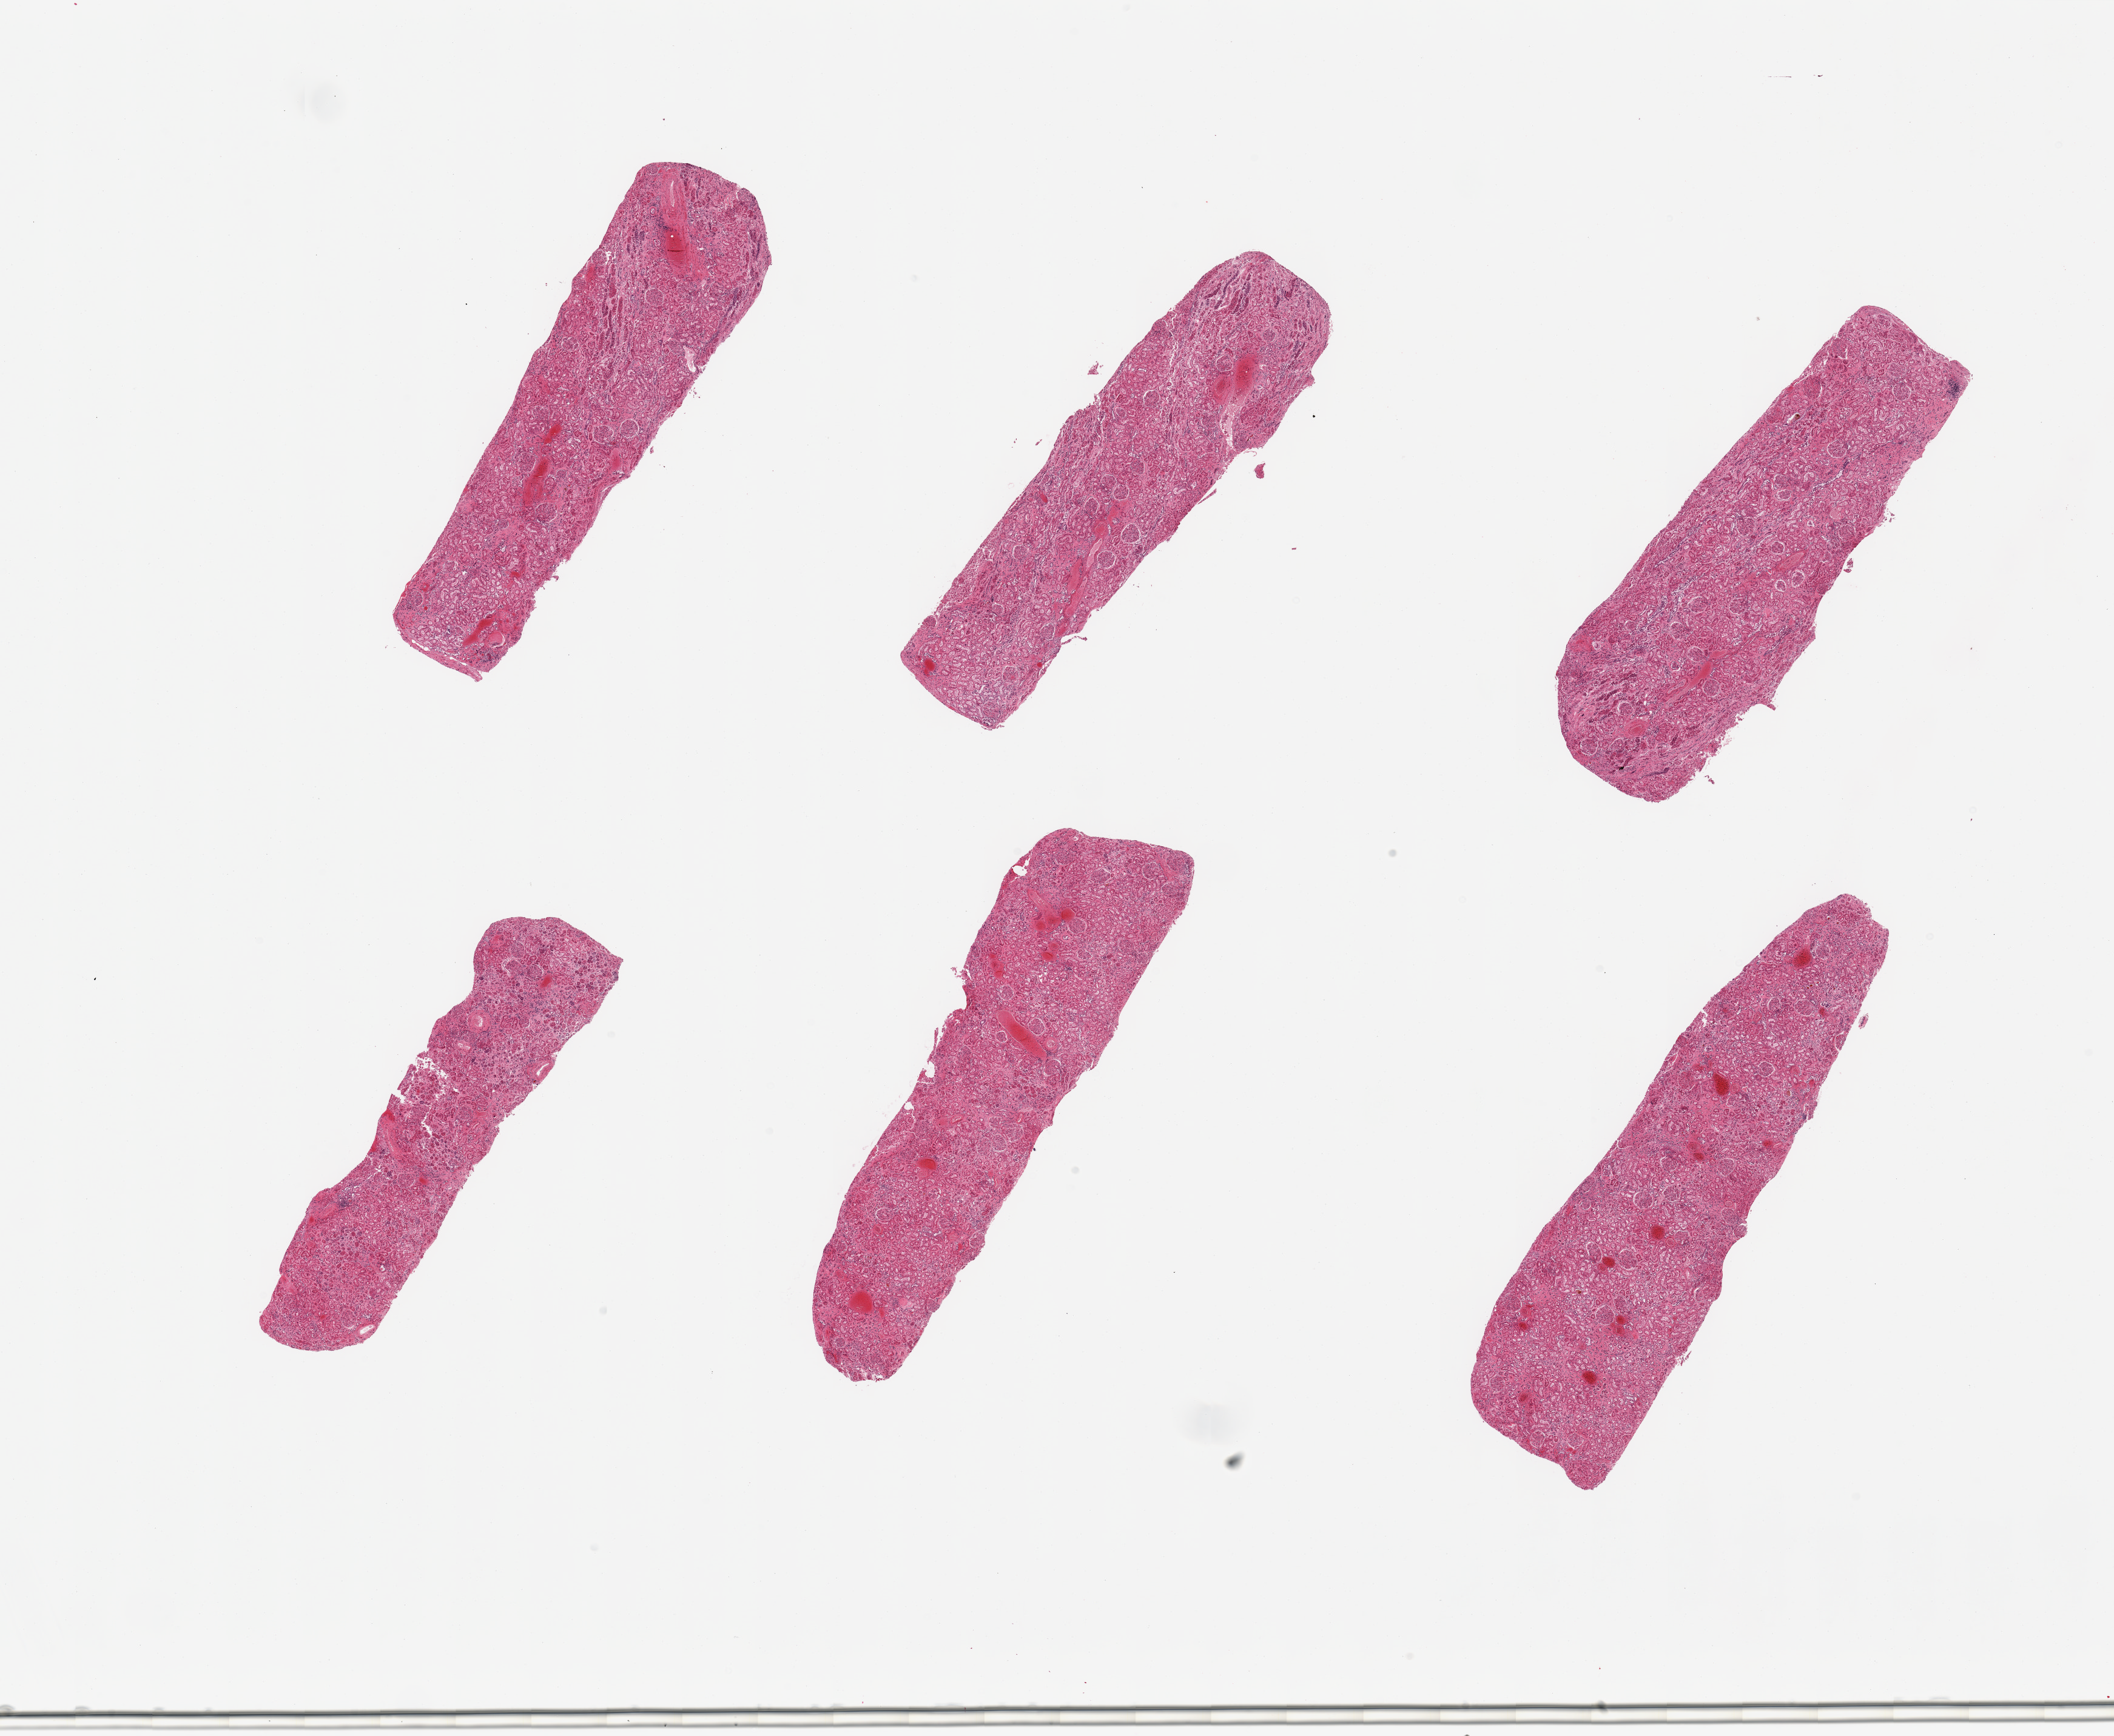
Whole-slide image, H&E stain, brightfield, shown as a low-resolution overview of the whole scanned area (about 27.6 x 22.6 mm). PAXgene-fixed paraffin-embedded (PFPE) section. Sampled site (target tissue): renal cortex. Tissue donor sample. Male donor.
Review note (as recorded): 6 pieces; moderate vascular congestion; no chronic lesions.